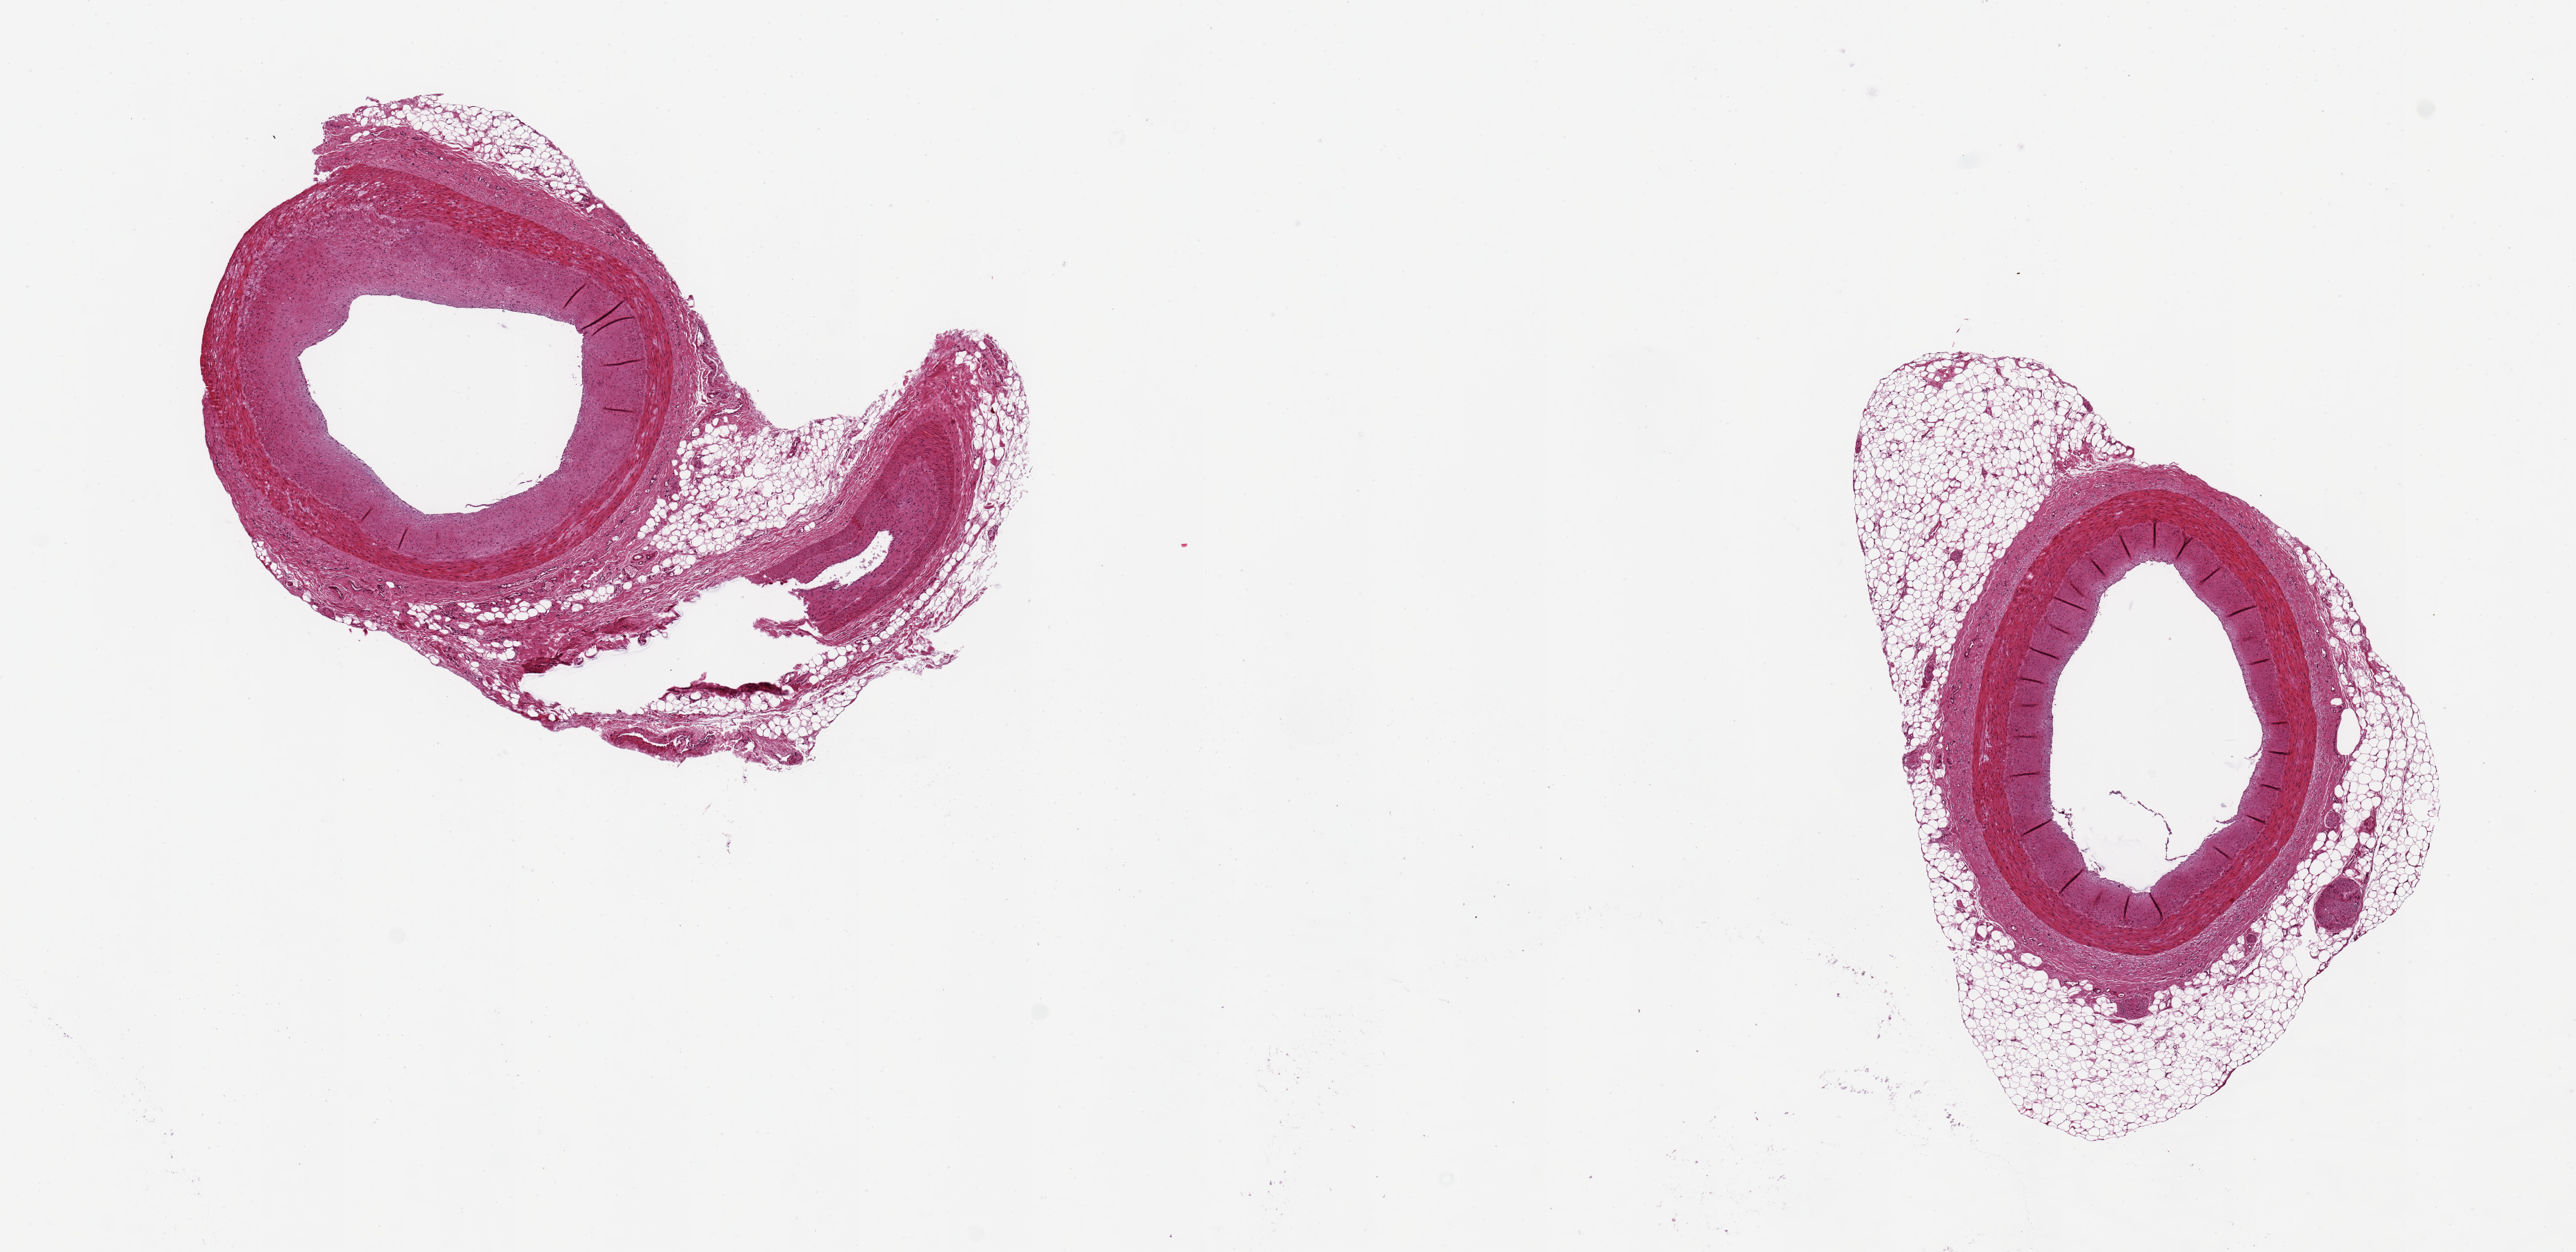
Hematoxylin and eosin (H&E) whole-slide image, brightfield — low-resolution overview of the scanned area, about 14.8 x 7.2 mm; PAXgene-fixed, paraffin-embedded tissue; target tissue: coronary artery; tissue donor sample. Female donor.
Pathologist's review note for this sample: 2 pieces, 2.8 & 2.9 mm arteries with up to 1 mm surrounding adipose.